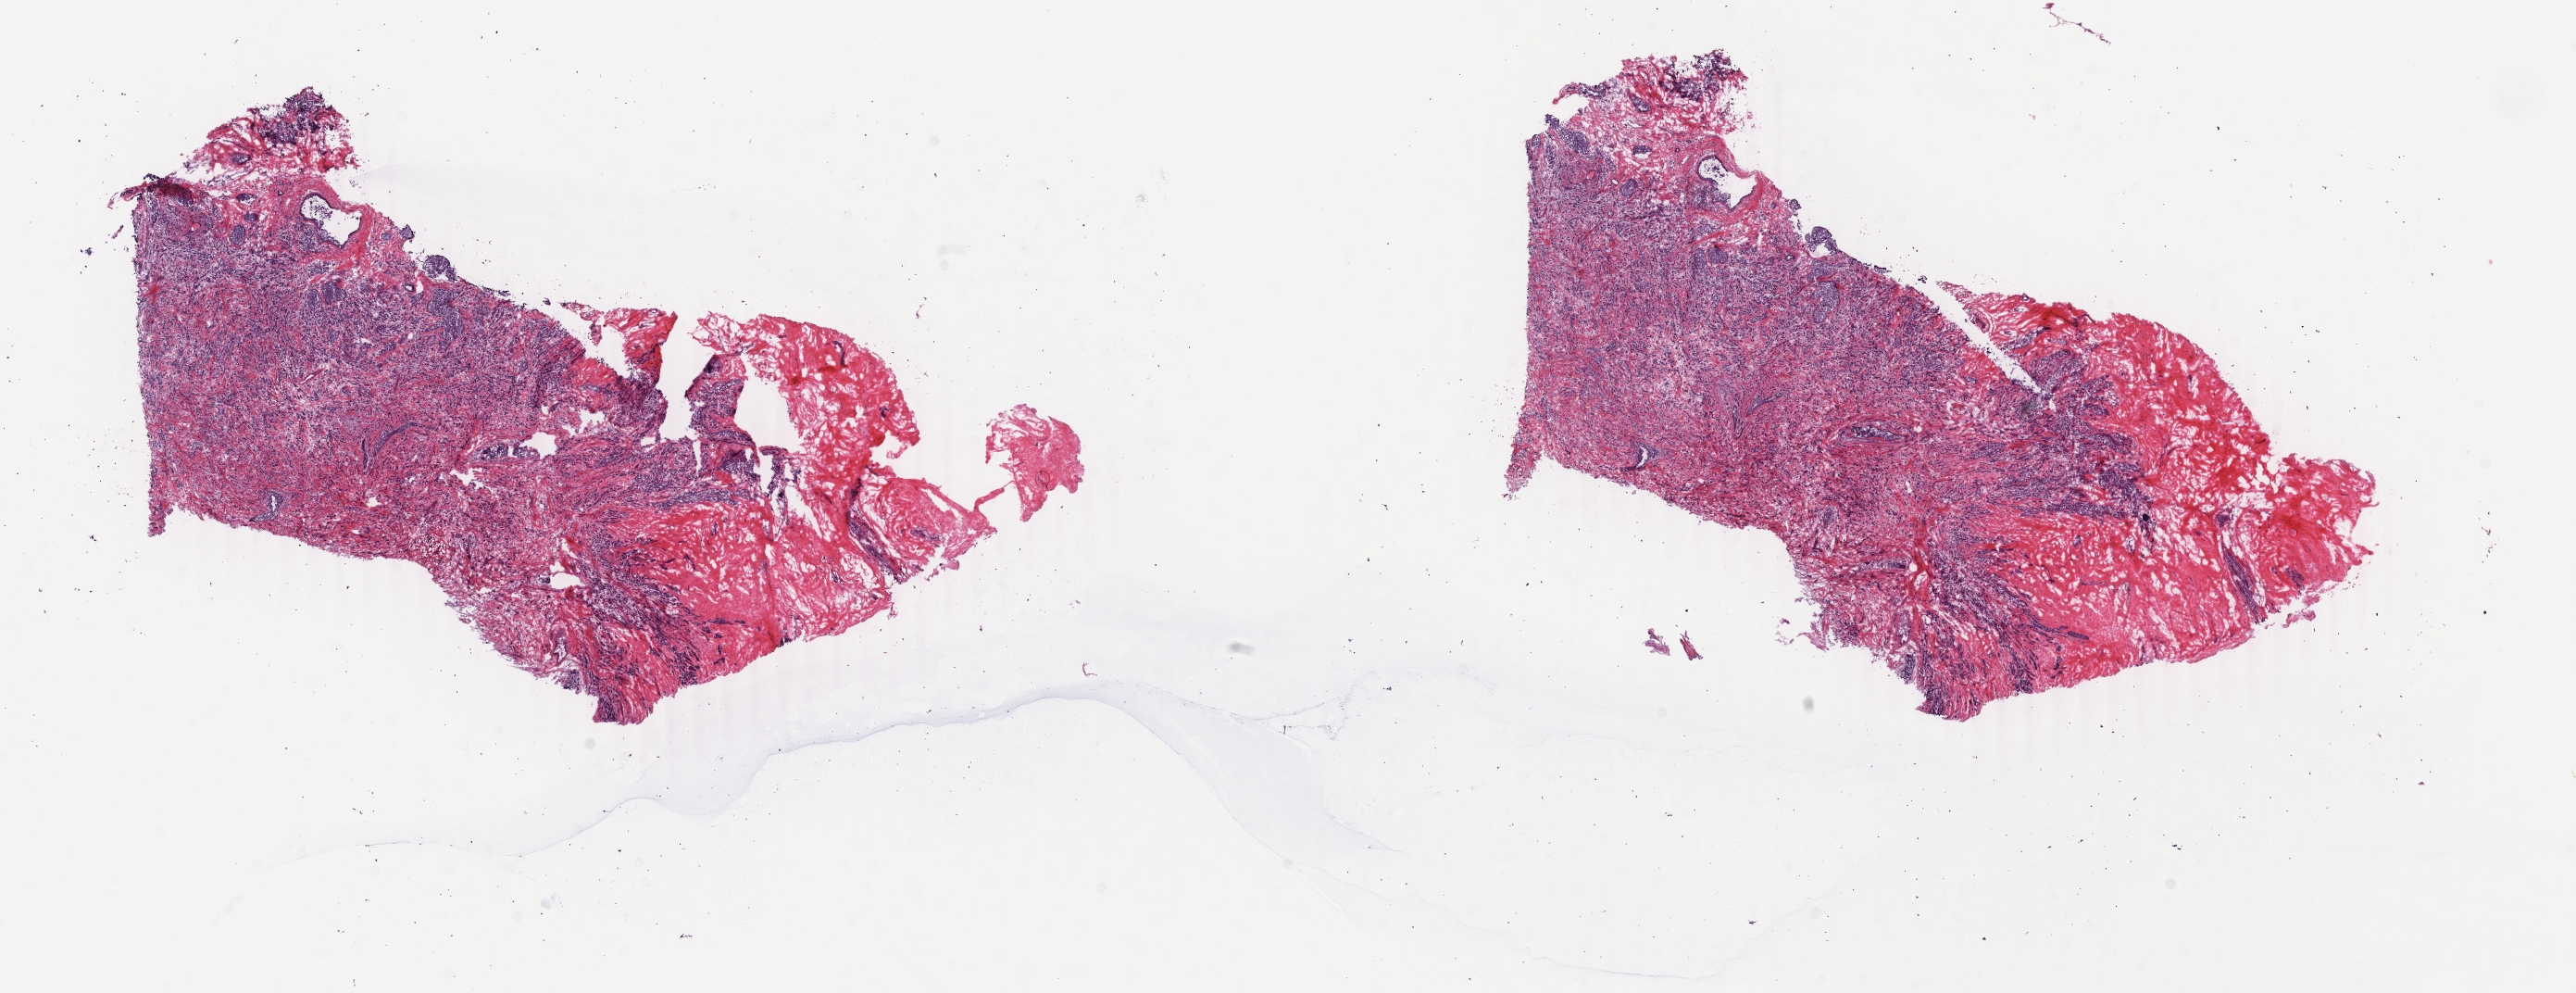
Whole-slide histology image, Hematoxylin and eosin (H&E) stained, low-resolution overview of the scanned area, about 22.1 x 8.5 mm (from a 40x scan), frozen section from the bottom of the tissue portion, breast, primary tumour sample. Female patient; age at initial diagnosis 75 years. Slide review estimates, as recorded: tumour cells 80%, tumour nuclei 80%, normal cells 2%, stromal cells 17%, necrosis 1%. Inflammatory infiltration, as recorded: lymphocyte infiltration 2%, monocyte infiltration 1%, neutrophil infiltration 0%.
Diagnosis: Pleomorphic carcinoma. Lymph nodes positive (case pathology): 0 of 4 examined. AJCC pathologic stage: IIA (6th edition).